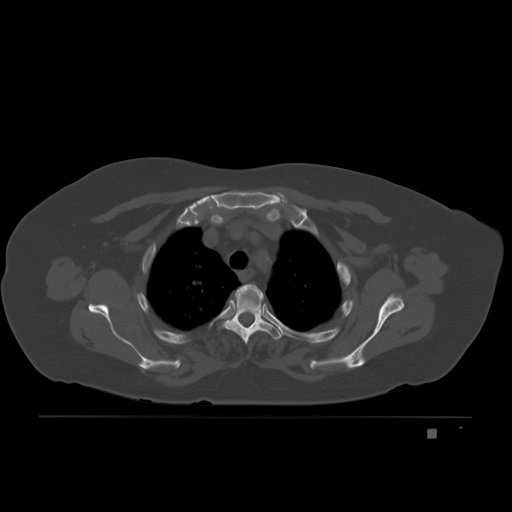
CT including the spine, one axial slice; slice 161 of 221 in the series (ordered by position); bone window (W 1800 / L 400 HU); 512 × 512 image matrix. Female patient, age 63 years. Case-level facts recorded for this patient, not image findings: primary cancer: breast.
Outlined on this slice (semi-automatic segmentation, software-assisted and operator-edited):
- T3 vertebra: bounding box [x1, y1, x2, y2] px = [221, 287, 281, 344]